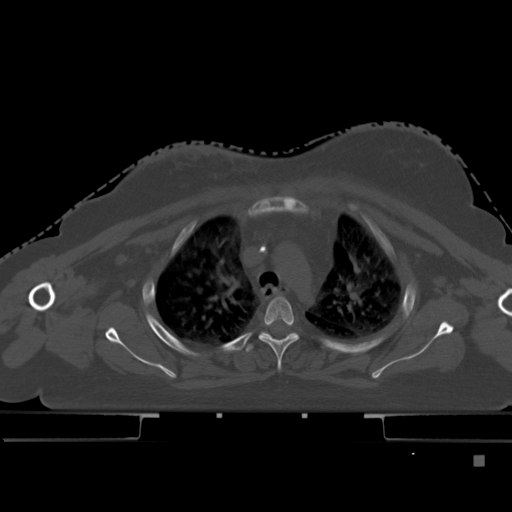
CT including the spine, one axial slice. Position 343 of 495 along the scan axis. Bone window (W 1800 / L 400 HU). 1.5 mm slice thickness. 512 × 512 image matrix, field of view 404 × 404 mm. Patient: female, 33 years. From the clinical record (not read from this slice): primary cancer: breast; vertebrae with lytic lesions (as recorded): T1.
Structures marked on this image (semi-automatically segmented with operator editing):
- T3 vertebra: bounding box [x1, y1, x2, y2] px = [259, 296, 299, 371]
- T4 vertebra: [245, 332, 299, 353]